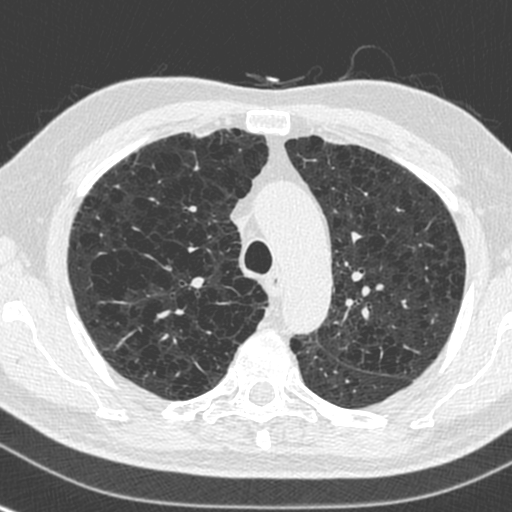
Axial slice from a low-dose chest CT screening exam; baseline screening round; lung window (W 1500 / L -600 HU); slice 67 of 250 in the series; 512 × 512 image matrix. Male, age 73 years at enrolment.
• Lesion marked by an expert reader, bounding box <147,247,195,286> (left, top, right, bottom; pixels).
• No non-calcified nodule or mass ≥4 mm was recorded by the screening reader at this exam.
• Official screen result: negative screen, significant abnormalities not suspicious for lung cancer.
• Lung cancer was diagnosed 446 days after this screen (after the second annual screen): squamous cell carcinoma, NOS, right upper lobe, stage IA (AJCC 6th edition), 10 mm at pathology.